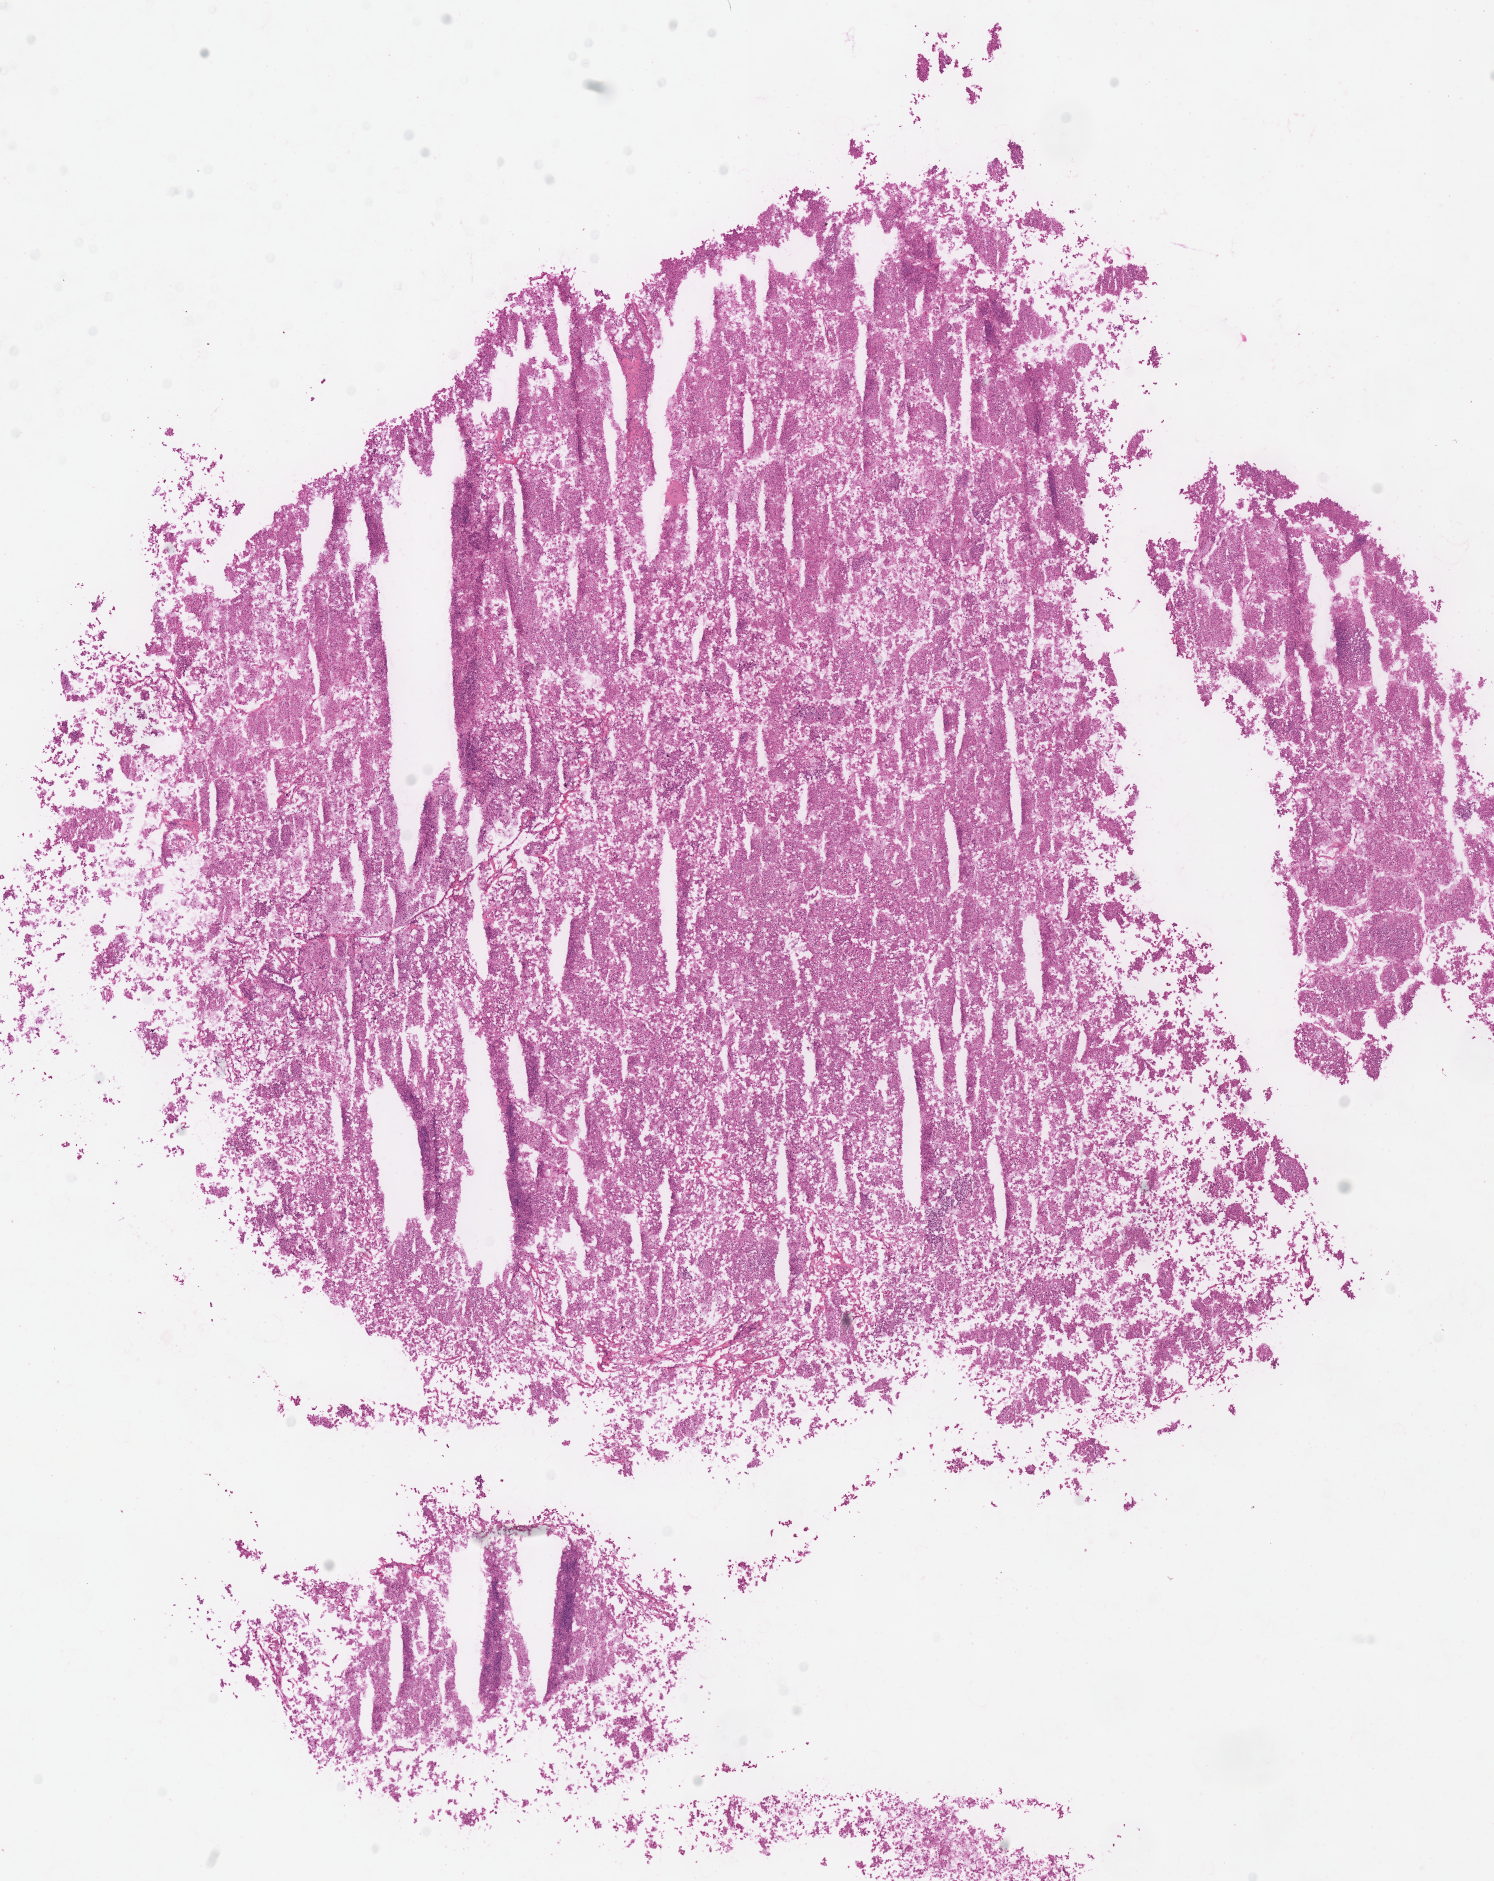
Whole-slide histology image, Hematoxylin and eosin (H&E) stained, shown as a low-resolution overview of the whole scanned area (about 11.7 x 14.8 mm), frozen section from the top of the tissue portion, kidney, primary tumour sample. Male, age 37 years at initial diagnosis. Slide review estimates, as recorded: tumour cells 90%, tumour nuclei 85%, normal cells 0%, stromal cells 10%, necrosis 0%.
Laterality: left. AJCC pathologic stage: III (6th edition). Diagnosis: Renal cell carcinoma, chromophobe type.